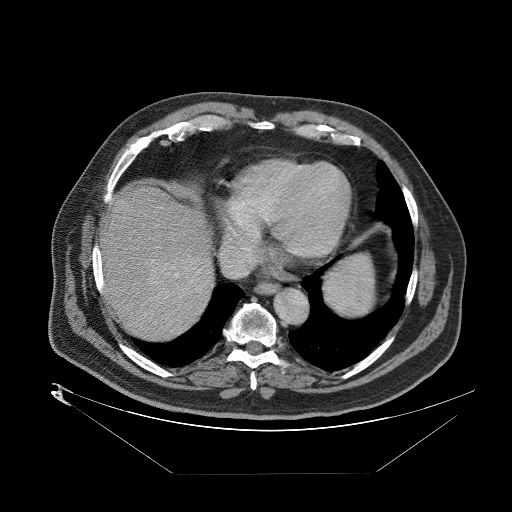
Contrast-enhanced abdominal CT (liver protocol), one axial slice; reconstruction kernel STANDARD; one of 2 acquisitions stored at this slice position; soft-tissue window (W 400 / L 40 HU); 2.5 mm slice thickness; 512 × 512 image matrix, field of view 480 × 480 mm. Case-level facts recorded for this patient, not image findings: diagnosis: hepatocellular carcinoma (patient treated with transarterial chemoembolisation; whether this scan precedes or follows treatment is not stated here); TNM stage (as recorded): Stage-II; Child-Pugh class: B; tumour nodularity: multinodular.
Annotated regions visible in this slice (semi-automatic segmentation, software-assisted and operator-edited):
- abdominal aorta: box from (x=273, y=288) to (x=308, y=323) px
- liver parenchyma outside the tumour (the mass and vessels are separate outlines, so this box may not span the whole liver): (x=99, y=180)–(x=210, y=332)
- mass: (x=144, y=252)–(x=210, y=314)
- liver vessels: (x=162, y=251)–(x=177, y=305)